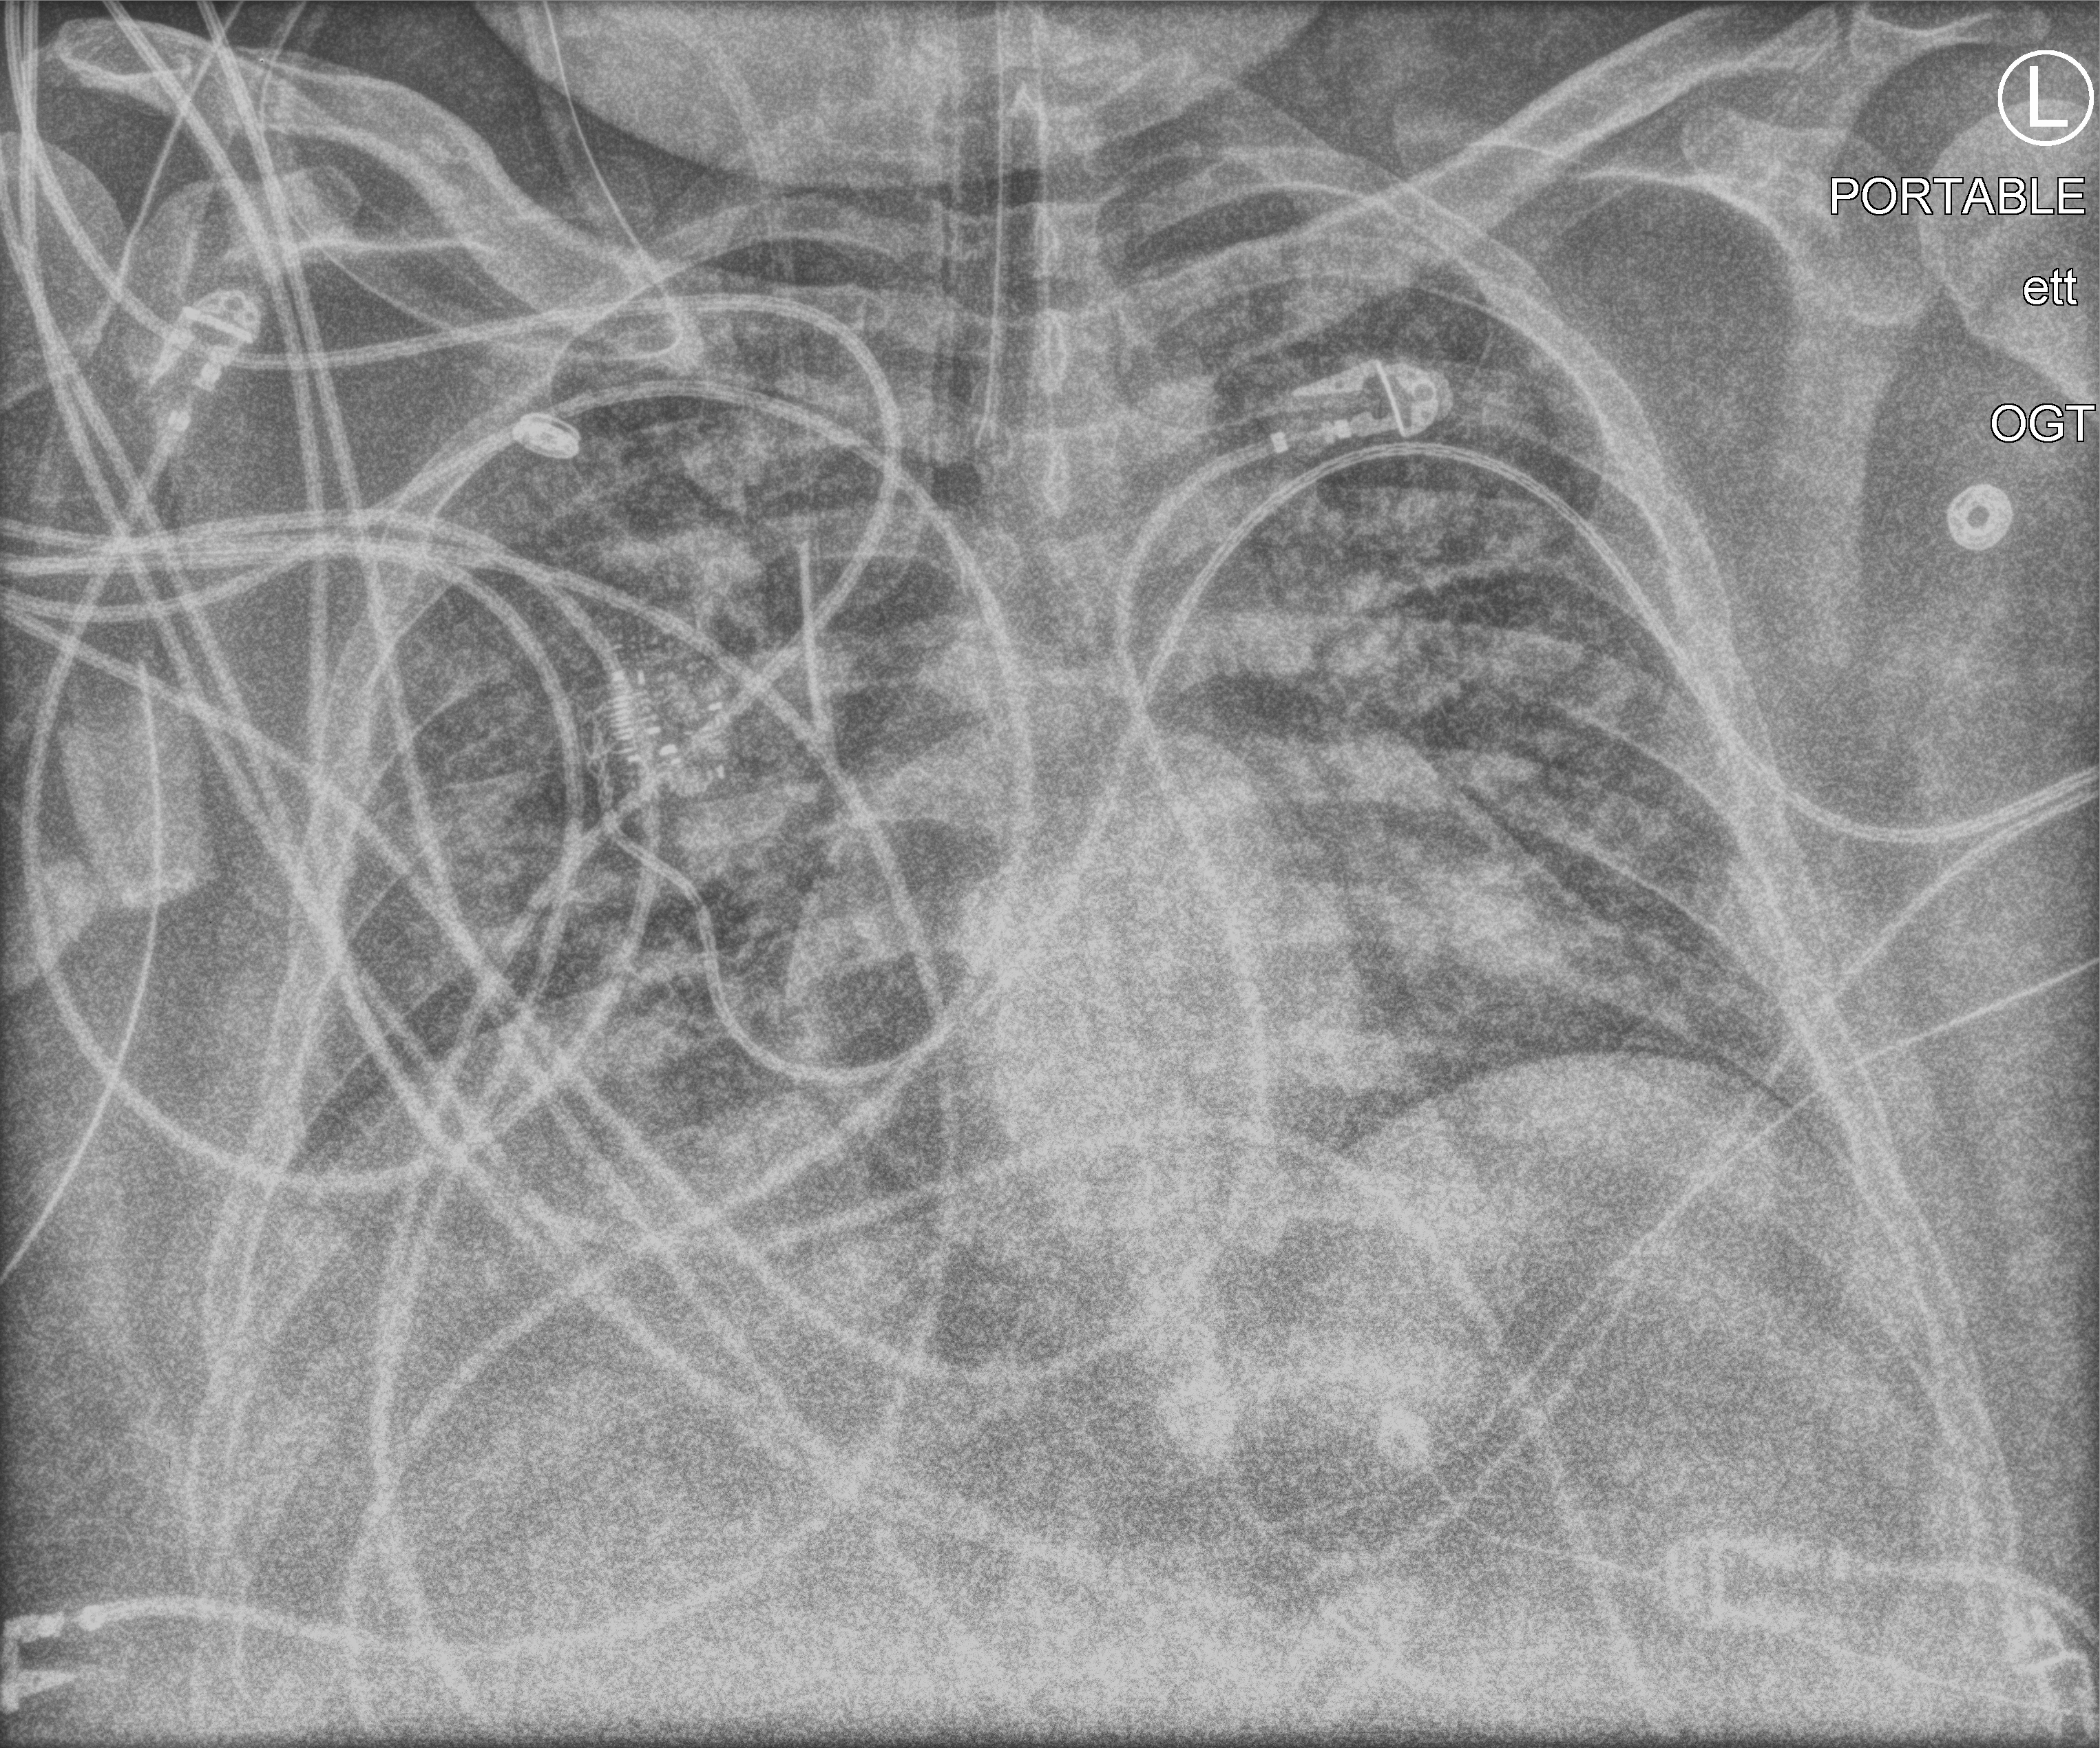
Portable chest radiograph; anteroposterior (AP) projection. Patient hospitalised with COVID-19, aged 18–59 years.
Admission-level facts for this patient (not findings on this image; timing relative to this image not recorded): admitted to intensive care during this hospital stay: yes.